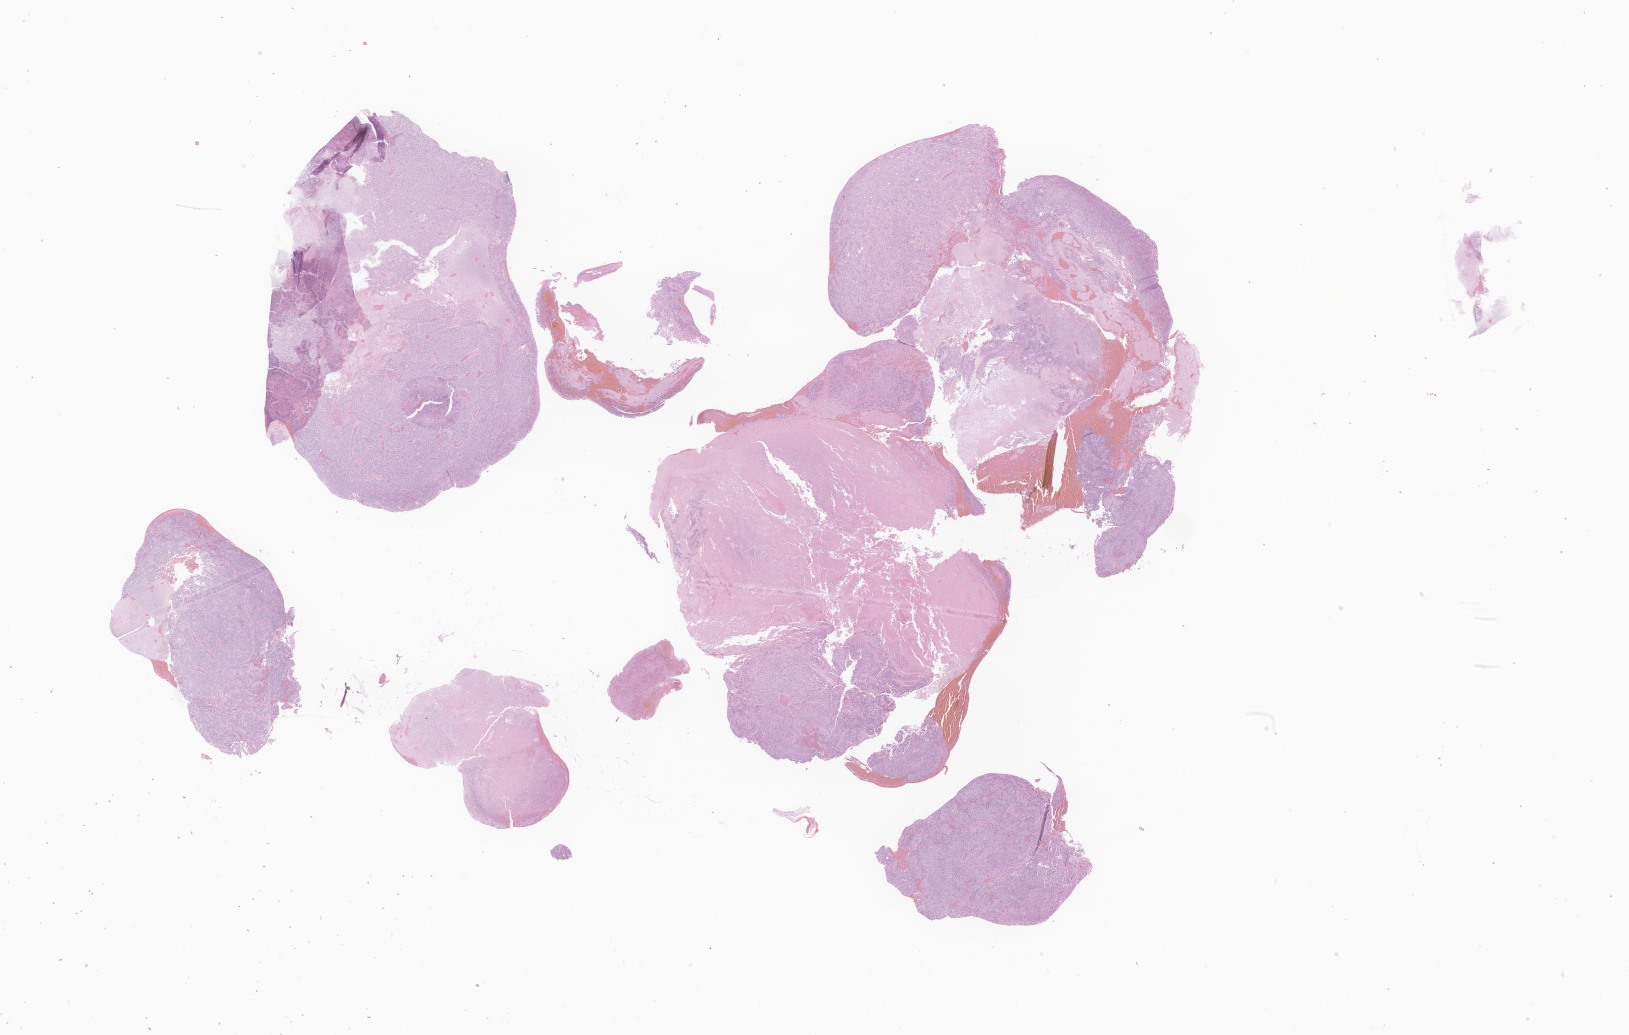
Digitized hematoxylin and eosin (H&E)-stained section of tumor tissue from the frontal lobe — shown as a low-resolution overview of the whole scanned area (about 27.5 x 17.5 mm), formalin-fixed paraffin-embedded section. Patient male; age 175 months (14 years 7 months).
• diagnosis (ICD-O-3 morphology term): Ependymoma, NOS